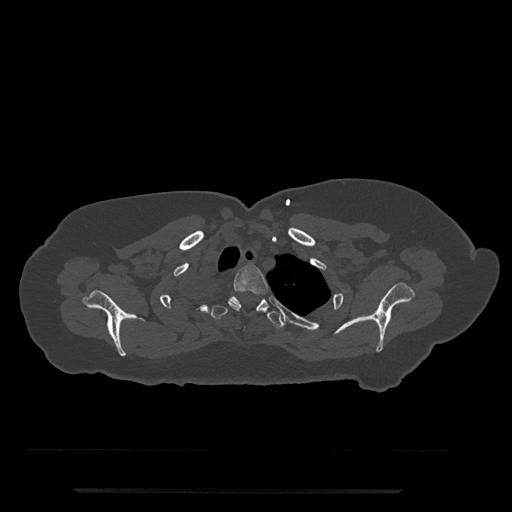
CT including the spine, one axial slice; position 656 of 797 along the scan axis; reconstruction kernel Br40s/3; 120 kVp; bone window (W 1800 / L 400 HU); 512 × 512 image matrix. Patient: female, 51 years. Case-level facts recorded for this patient, not image findings: primary cancer: neuro.
Annotated regions visible in this slice (semi-automatic segmentation, software-assisted and operator-edited):
- T2 vertebra: bounding box (x1, y1, x2, y2) in pixels: (228, 265, 269, 311)
- T3 vertebra: (211, 296, 285, 328)